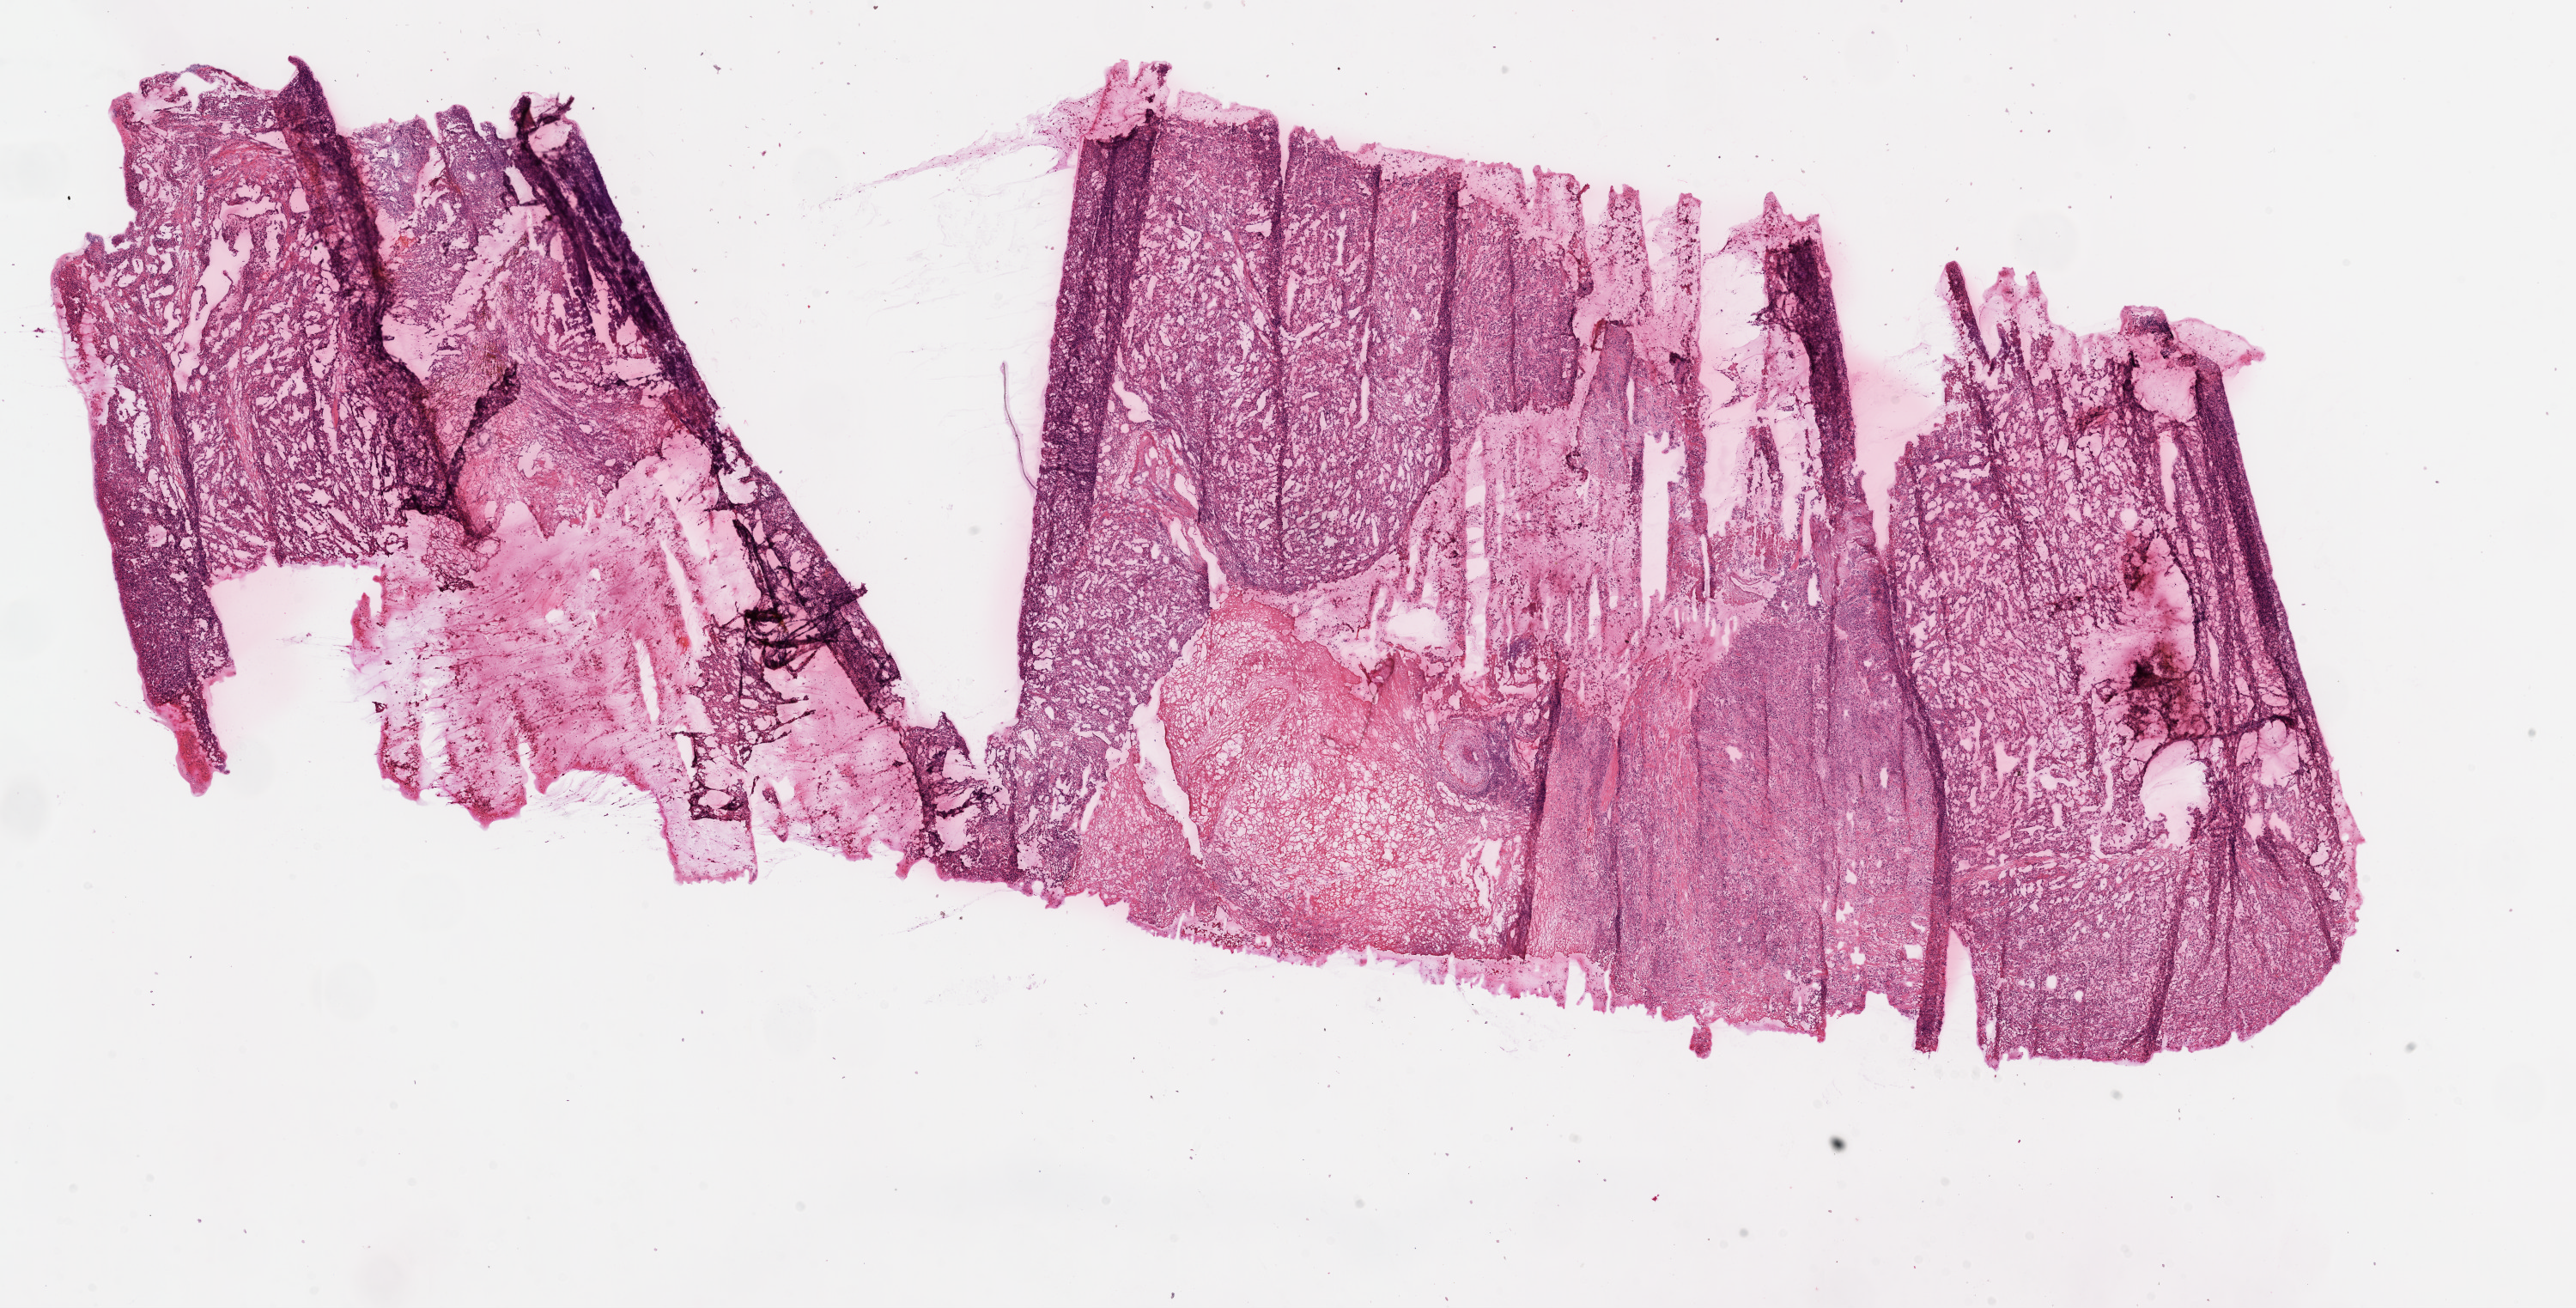
Digitized H&E-stained tissue section (whole slide) — low-resolution overview of the scanned area, about 24.1 x 12.2 mm. Frozen section from the top of the tissue portion. Primary tumour sample from the kidney. Patient: female, age at initial diagnosis 63 years. Histologic grade: G4 (undifferentiated). Pathologist review of this section (percent, as recorded): tumour cells 90%, tumour nuclei 85%, normal cells 0%, stromal cells 10%, necrosis 10%.
Diagnosis: Clear cell adenocarcinoma, NOS. AJCC pathologic stage: IV. Laterality: left.